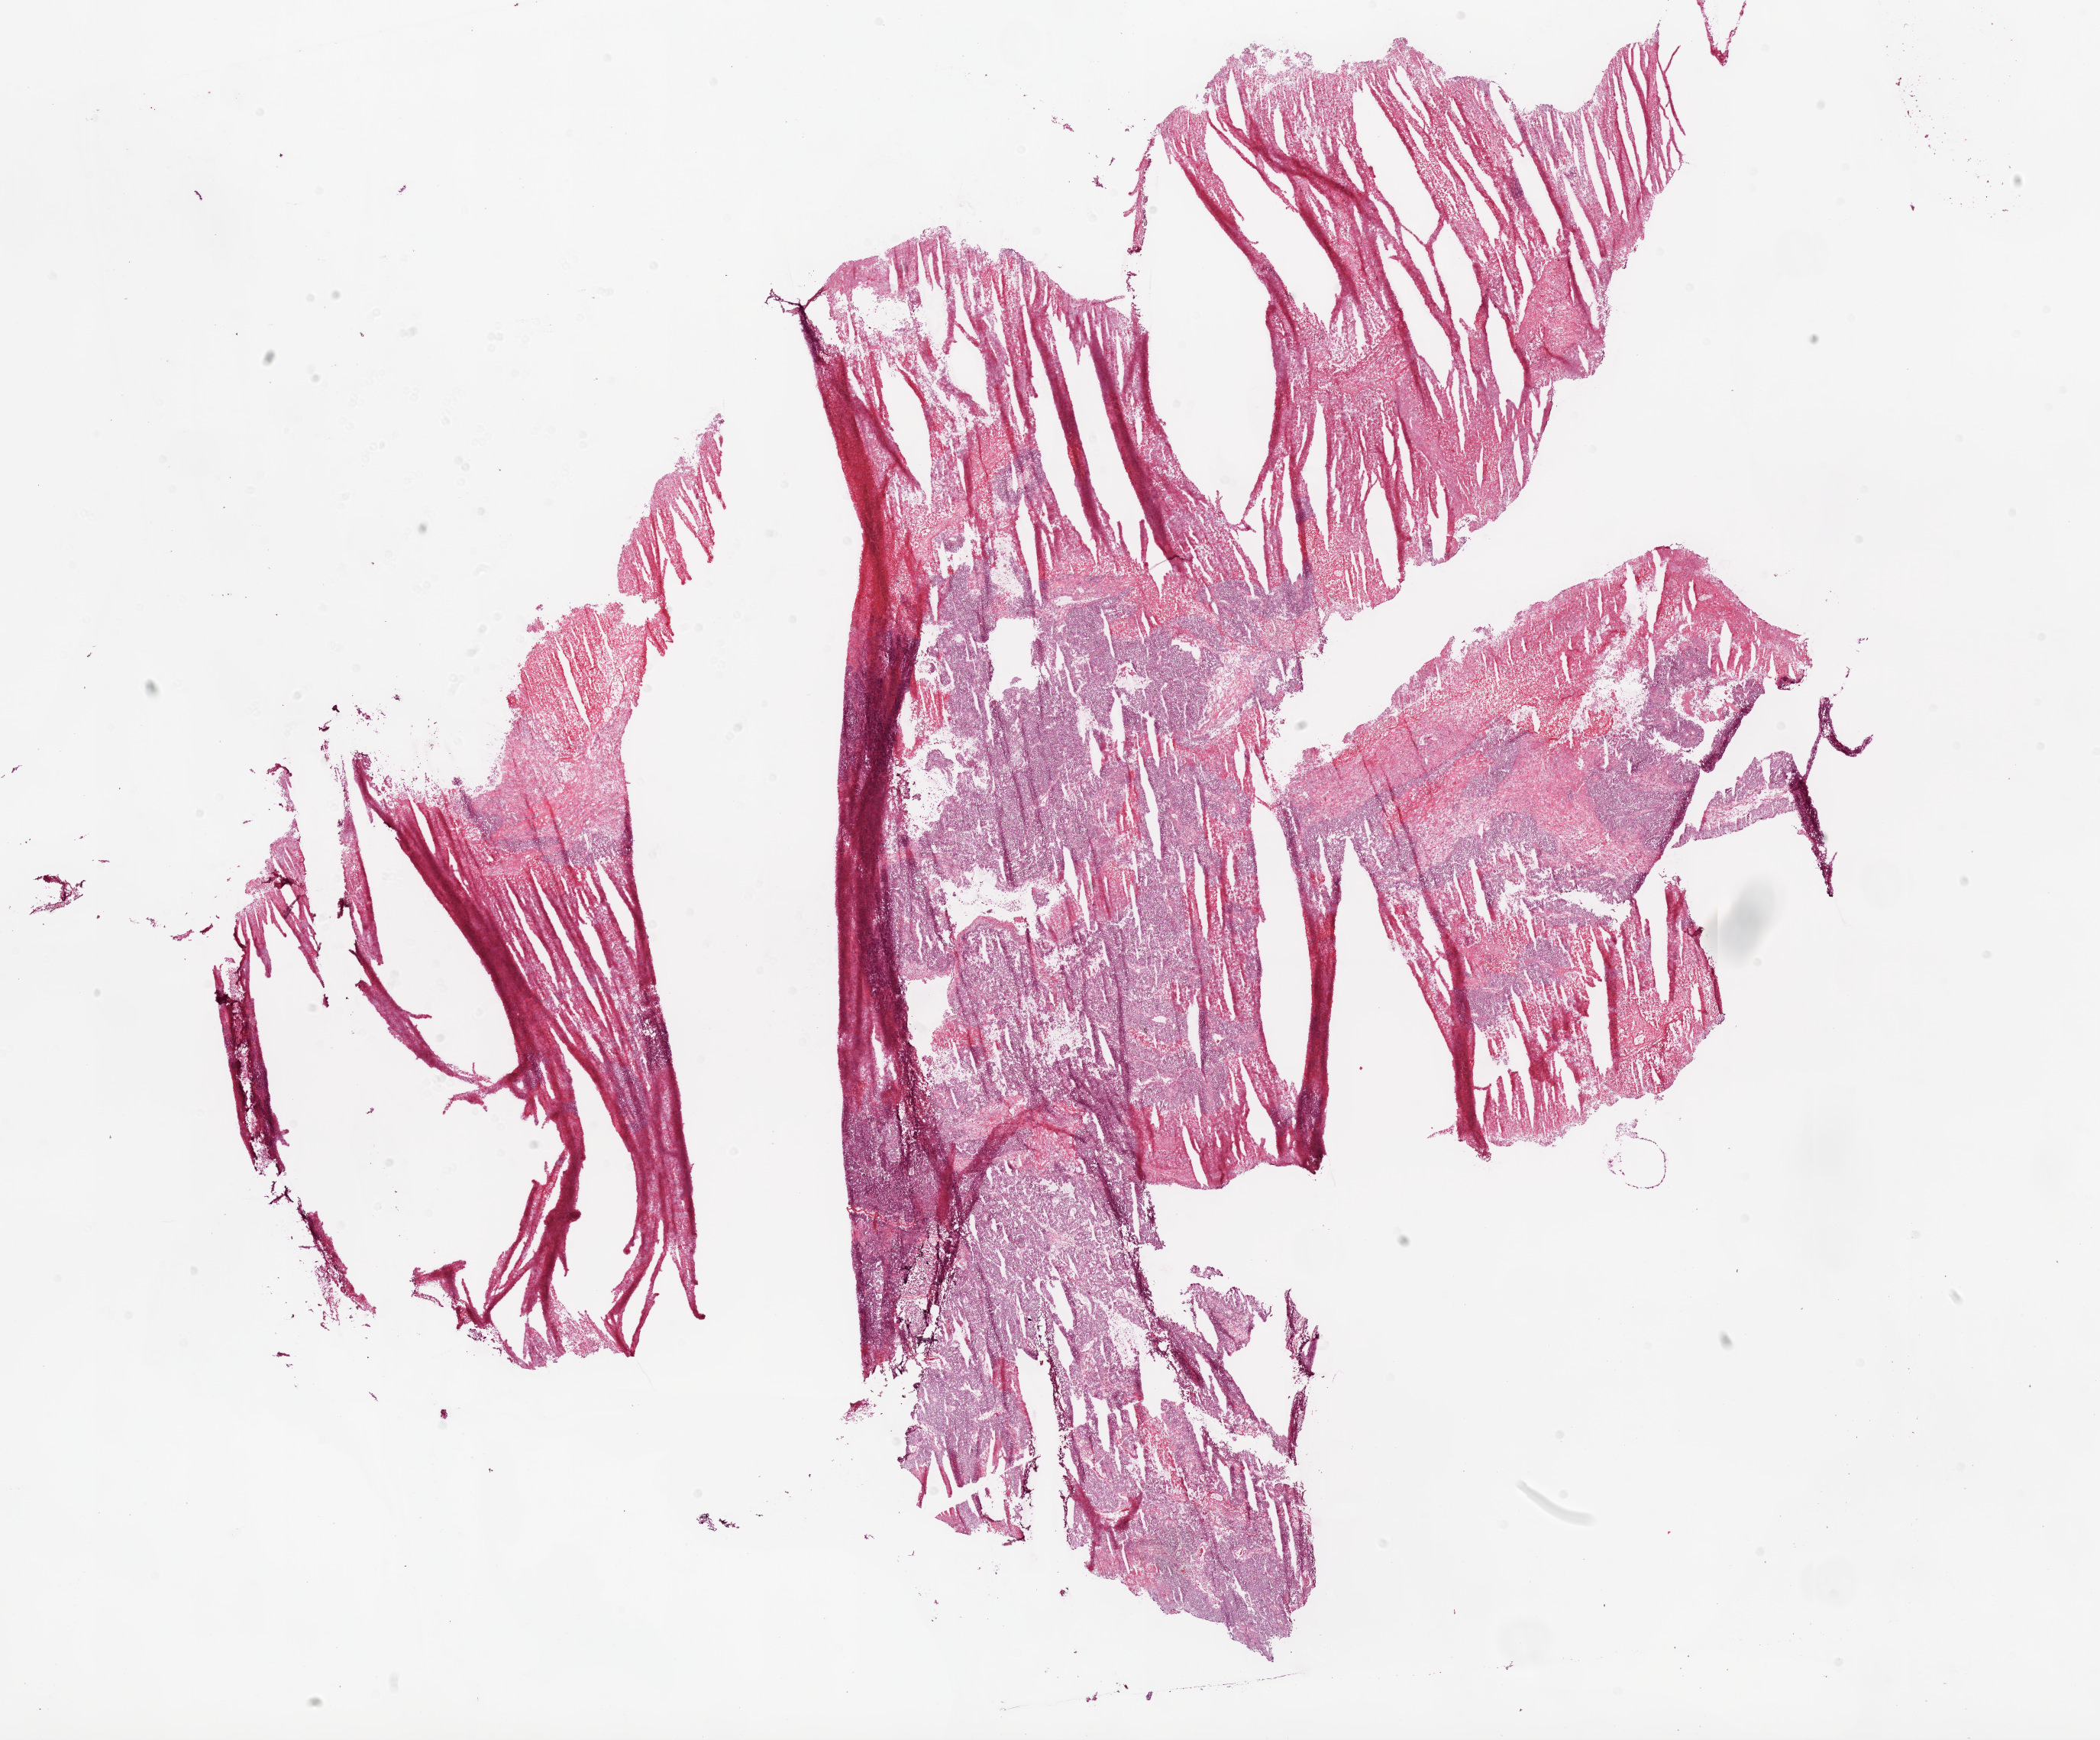
H&E-stained whole-slide image, whole scanned area (about 22.1 x 18.3 mm) shown as a low-resolution overview, frozen section from the bottom of the tissue portion, recurrent tumour sample from the ovary. Female patient; age at initial diagnosis 59 years. Slide review estimates, as recorded: tumour cells 80%, tumour nuclei 80%, normal cells 0%, stromal cells 10%, necrosis 10%. Infiltration values recorded for this section: lymphocyte infiltration 0%, monocyte infiltration 0%, neutrophil infiltration 10%.
This section: recurrent tumour. Patient diagnosis: Serous cystadenocarcinoma, NOS.